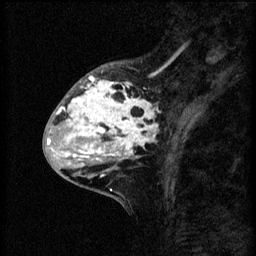
Breast MRI (dynamic contrast-enhanced), one sagittal slice. Position 22 of 60 along the scan axis. 3 images stored at this slice position (order not interpretable as contrast timing). 1.5 T. TE 4.2 ms, TR 8.2 ms. 256 × 256 image matrix, field of view 180 × 180 mm. Patient: female, 41 years.
Structures marked on this image (semi-automatic segmentation, software-assisted and operator-edited):
- analysis volume of interest (the breast-tissue region the enhancement analysis was run in; not a lesion): box from (x=53, y=62) to (x=160, y=175) px
- tumour enhancement mask (voxels above the 70 % enhancement threshold inside the analysis volume of interest): (x=56, y=76)–(x=160, y=175)